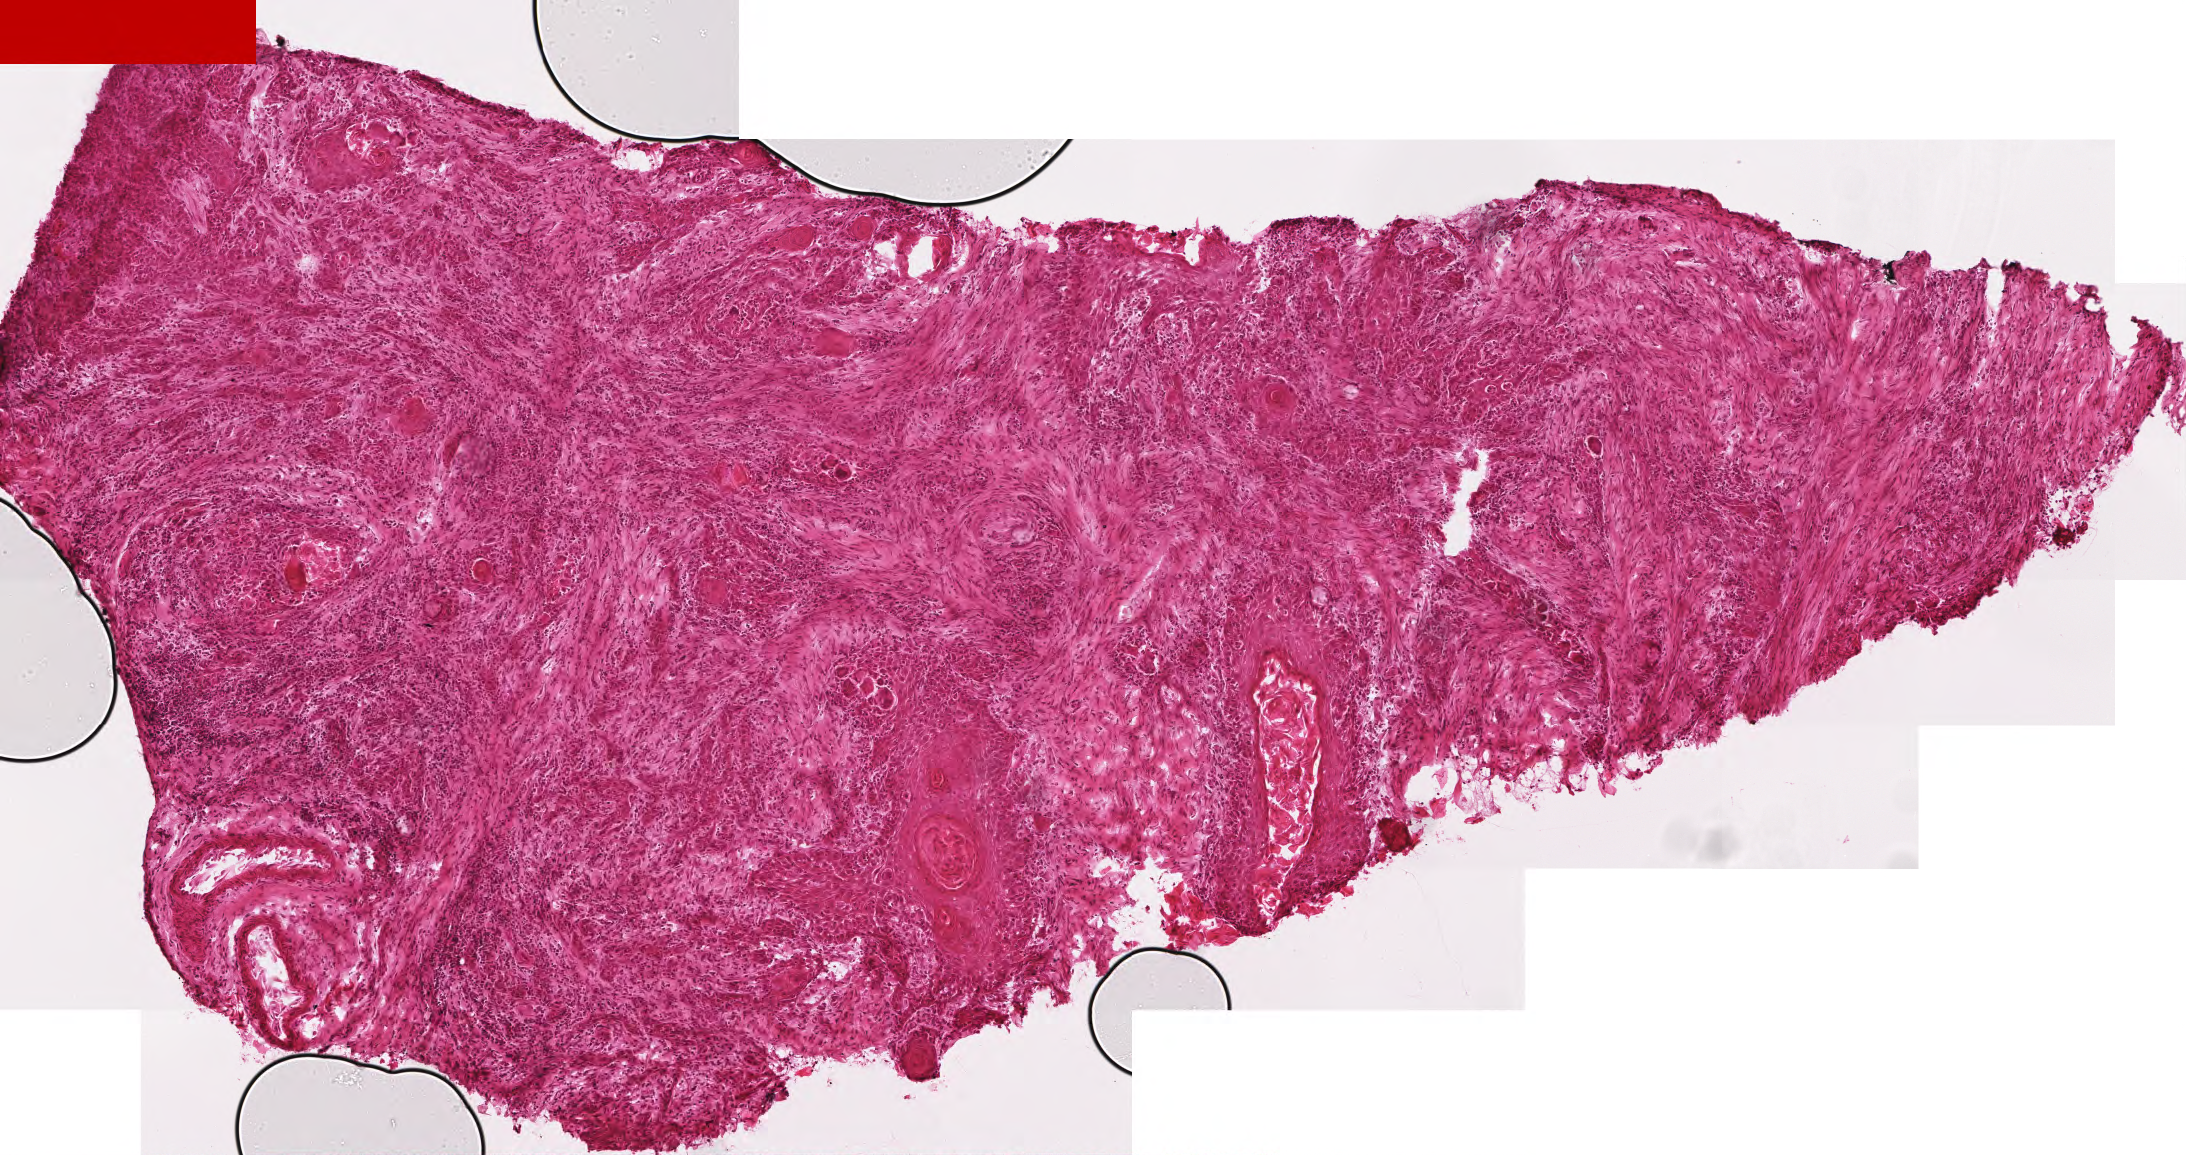
Digitized H&E-stained tissue section (whole slide) — low-resolution overview of the scanned area, about 4.4 x 2.3 mm, frozen section, head and neck, primary tumour sample. Male, age 83 years at initial diagnosis. Histologic grade: G2 (moderately differentiated). Pathologist review of this section (percent, as recorded): tumour cells 95%, tumour nuclei 60%, normal cells 0%, stromal cells 5%, necrosis 0%.
Diagnosis: Squamous cell carcinoma, NOS. AJCC pathologic stage: III (6th edition).